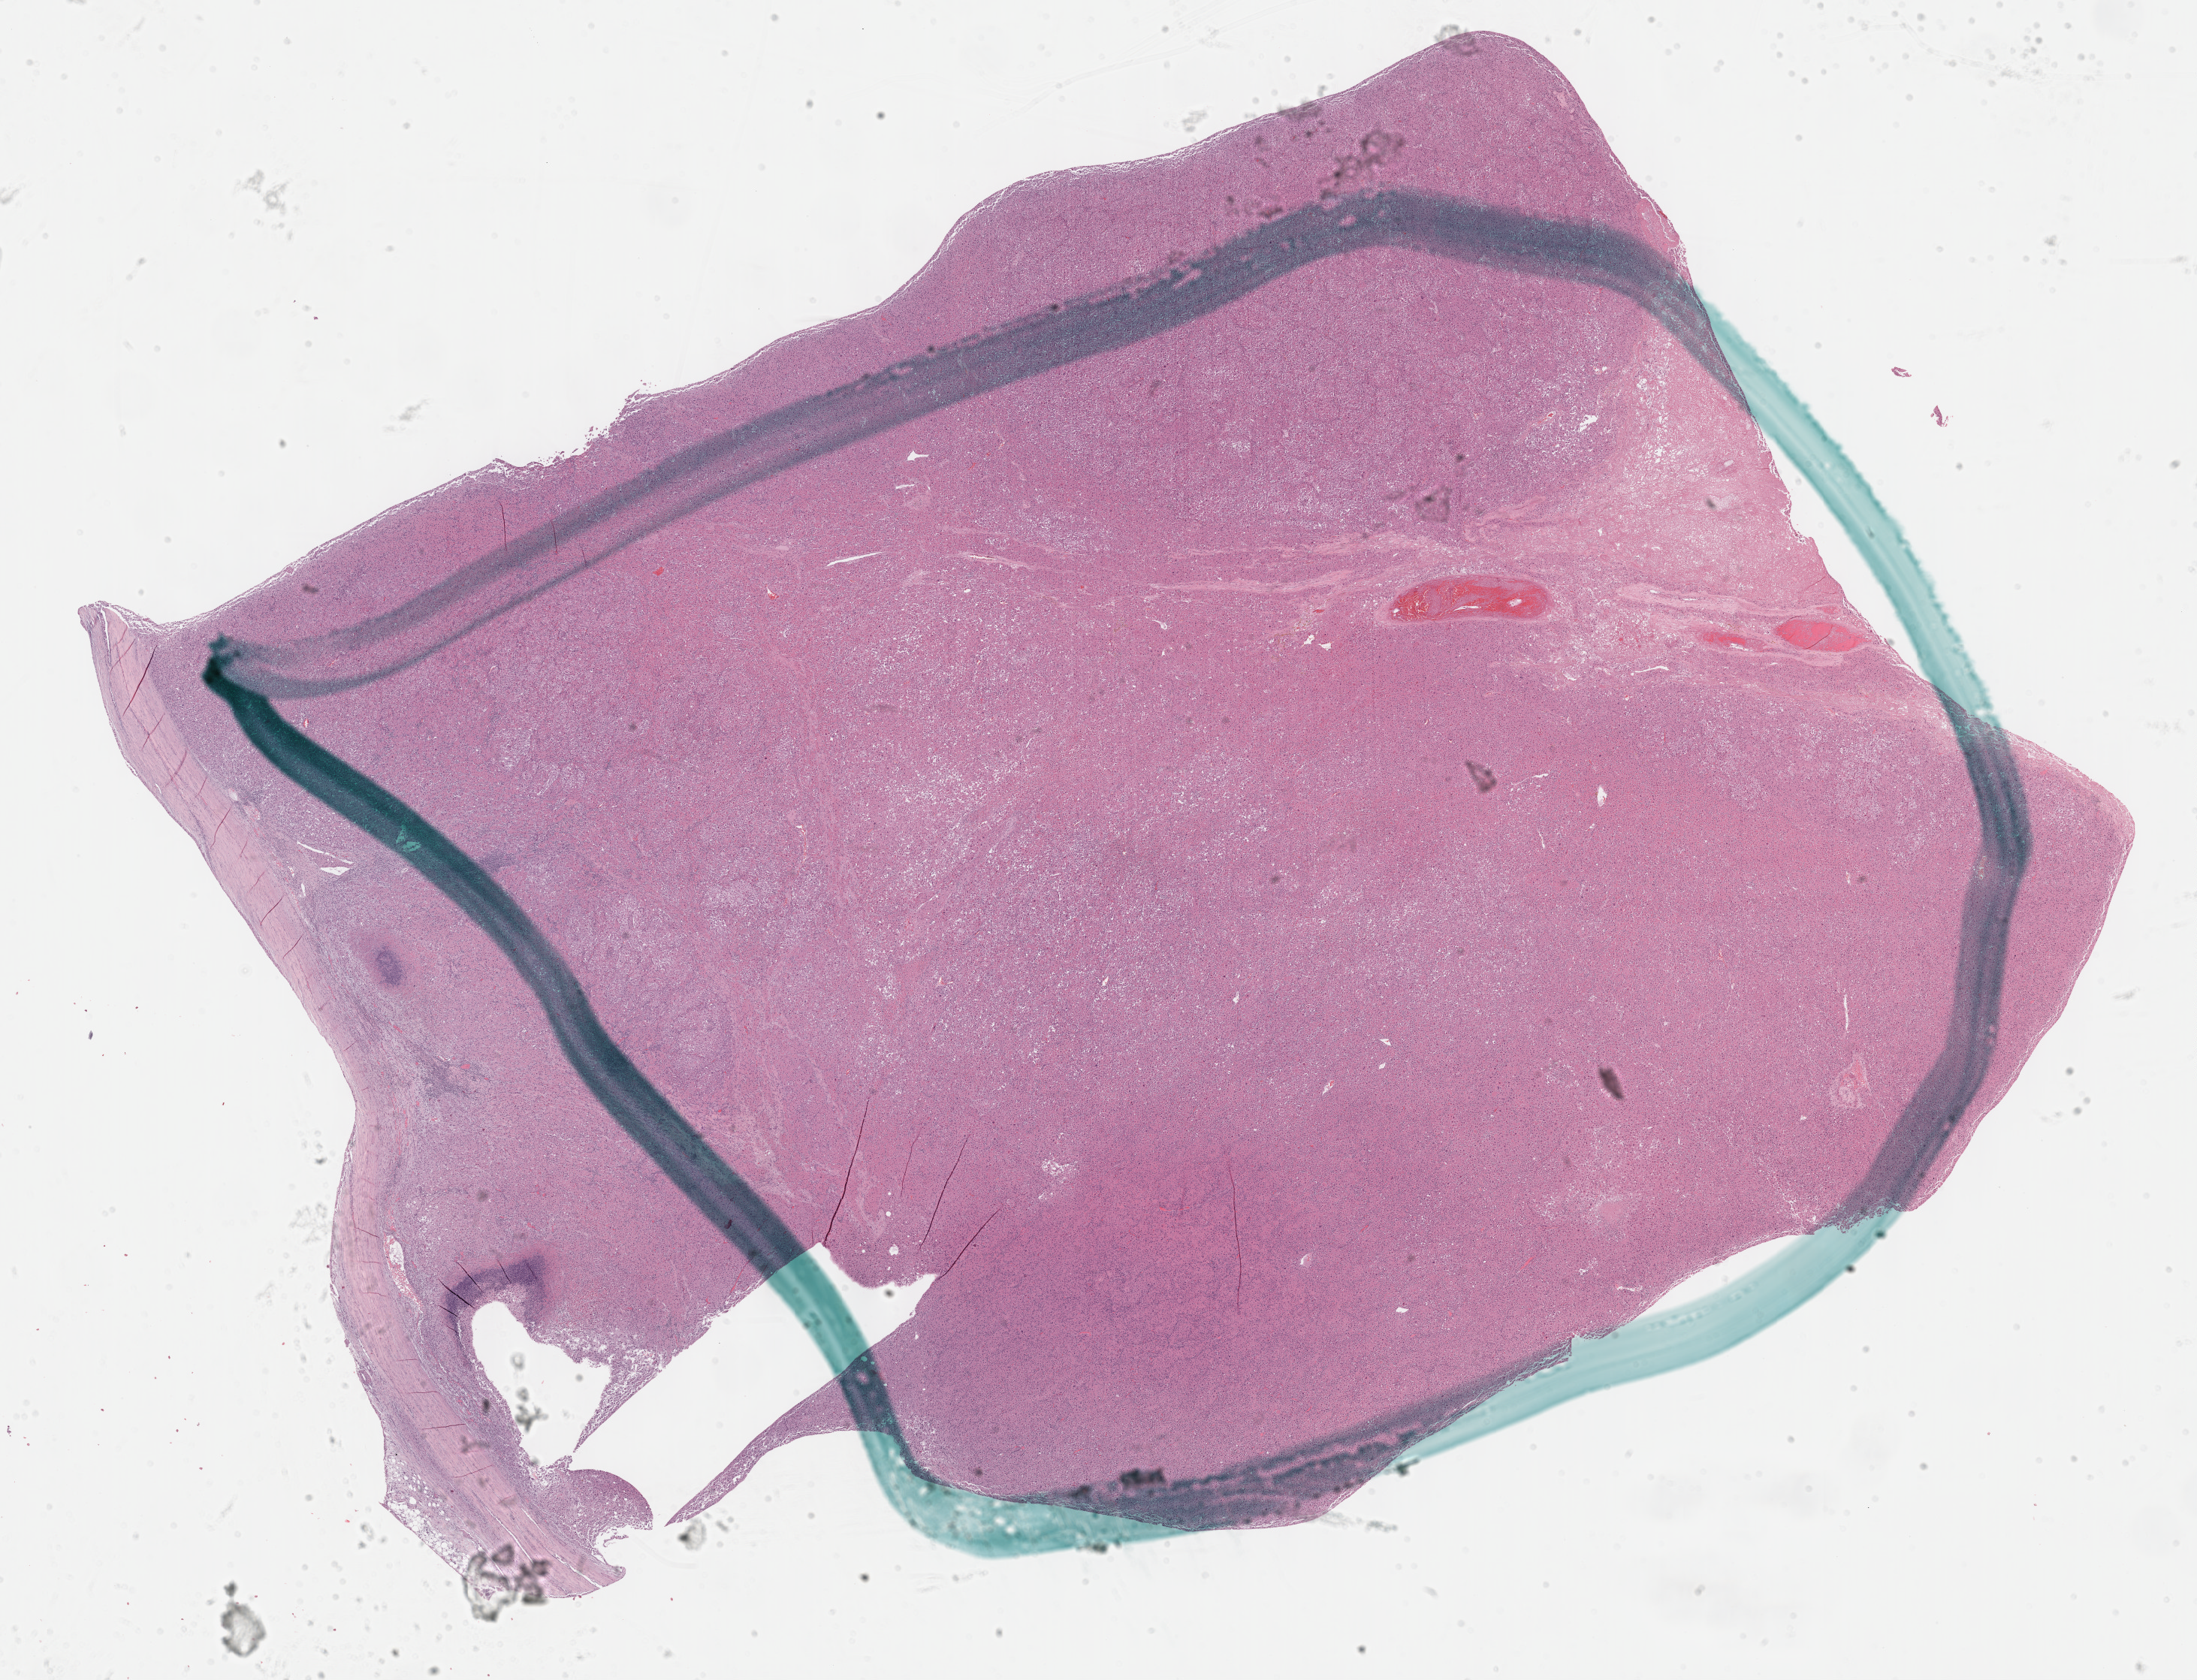
Digitized H&E tissue section (whole slide), a low-resolution overview of the entire scanned area, about 23.7 x 18.1 mm; formalin-fixed paraffin-embedded (FFPE) diagnostic section; sample: primary tumour, adrenal cortex. Male patient; age at initial diagnosis 55 years.
Histologic diagnosis: Adrenal cortical carcinoma.